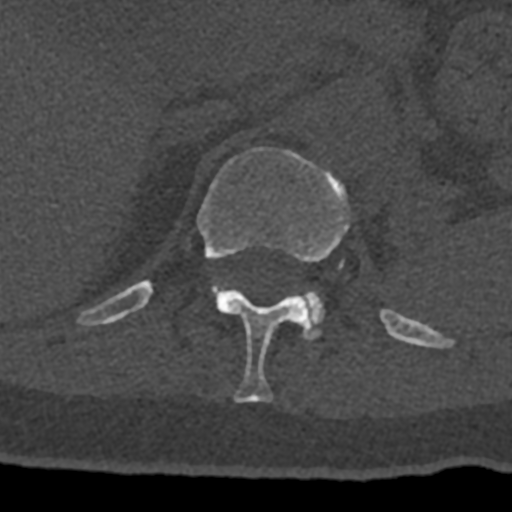
CT including the spine, one axial slice. Reconstruction kernel Br40s/3. 120 kVp. Bone window (W 1800 / L 400 HU). 512 × 512 image matrix. Male patient, age 74 years. Case-level facts recorded for this patient, not image findings: primary cancer: renal; vertebrae with lytic lesions (as recorded): T10, L1, L2, L3, L4, L5.
Structures marked on this image (semi-automatically segmented with operator editing):
- L1 vertebra: bounding box [x1, y1, x2, y2] px = [303, 291, 324, 339]
- T12 vertebra: [78, 147, 432, 403]